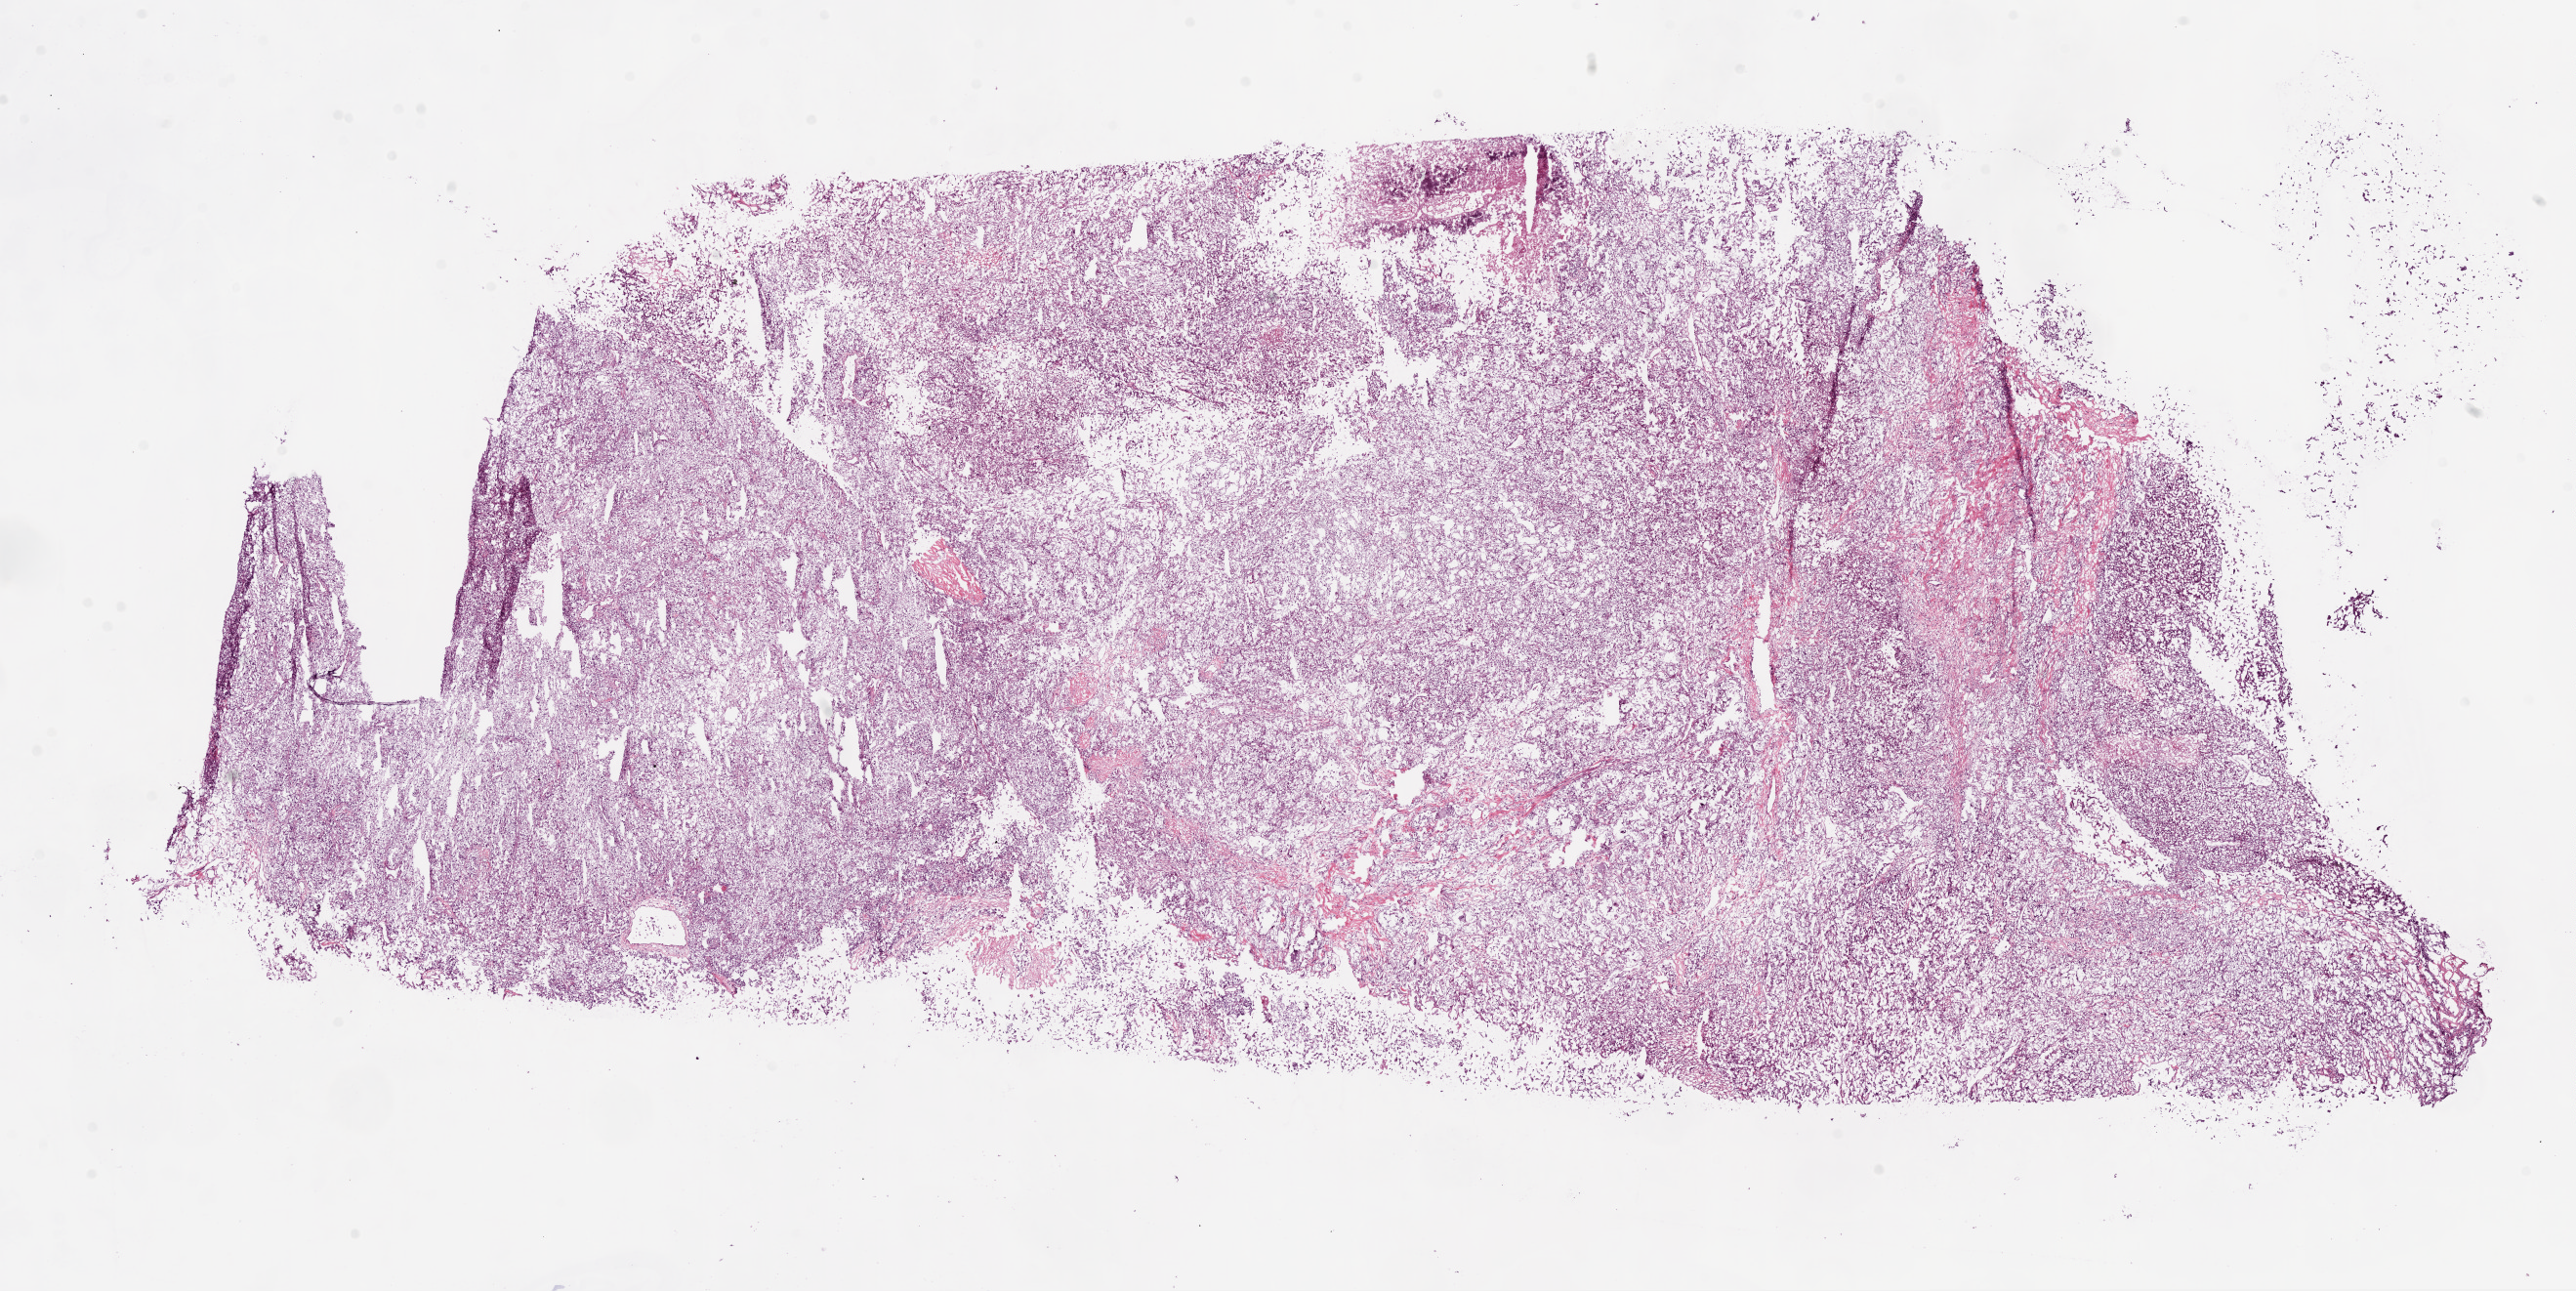
Whole-slide histology image, Hematoxylin and eosin (H&E) stained — a low-resolution overview of the entire scanned area, about 21.3 x 10.7 mm (slide scanned at 20x). Frozen section from the top of the tissue portion. Kidney, primary tumour sample. Male, age 73 years at initial diagnosis. Histologic grade: G4 (undifferentiated). Slide review estimates, as recorded: tumour cells 87%, tumour nuclei 85%, normal cells 0%, stromal cells 10%, necrosis 3%.
* AJCC pathologic stage: III
* TNM: T3b NX M0
* diagnosis: Clear cell adenocarcinoma, NOS